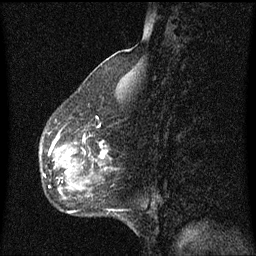
Breast MRI (dynamic contrast-enhanced), one sagittal slice; position 25 of 60 along the scan axis; dynamic contrast-enhanced series, image 2 of 3 at this slice position (ordered by acquisition); 1.5 T; TE 4.2 ms, TR 8.4 ms; 2 mm slice thickness; 256 × 256 image matrix, field of view 200 × 200 mm. Patient: female, 49 years. Case-level facts recorded for this patient, not image findings: setting: breast cancer imaged before/during neoadjuvant chemotherapy; receptor status: HR-positive, HER2-negative.
Annotated regions visible in this slice (semi-automatic segmentation, software-assisted and operator-edited):
- analysis volume of interest (the breast-tissue region the enhancement analysis was run in; not a lesion): box from (x=41, y=138) to (x=95, y=199) px
- tumour enhancement mask (voxels above the 70 % enhancement threshold inside the analysis volume of interest): (x=67, y=154)–(x=71, y=173)